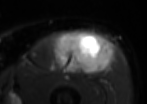
MRI of an extremity soft-tissue mass, one axial slice. Slice 44 of 85 in the series (ordered by position). T2-weighted fat-saturated. MR volume resampled by the dataset authors to the PET/CT grid (not the native acquisition matrix). 3.27 mm slice thickness. 147 × 104 image matrix. Male patient. Case-level facts recorded for this patient, not image findings: histological type: extraskeletal osteosarcoma; grade: high; site of the primary tumour: thigh.
Outlined on this slice (expert contour drawn on MRI and transferred to this co-registered scan by the dataset authors):
- gross tumour volume (mass): box from (x=56, y=30) to (x=109, y=75) px